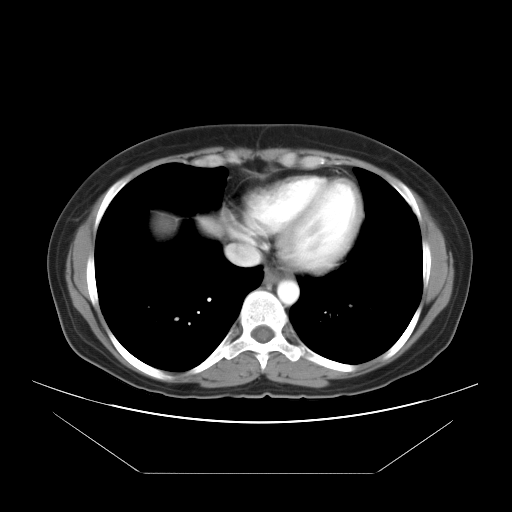
Contrast-enhanced abdominal CT, one axial slice; slice 34 of 34 in the series (ordered by position); reconstruction kernel STANDARD; 120 kVp; intravenous contrast given; soft-tissue window (W 400 / L 40 HU); 7.5 mm slice thickness; 512 × 512 image matrix. Female patient, age 38 years. From the clinical record (not read from this slice): diagnosis: colorectal cancer liver metastases, imaged before liver resection; multiple liver metastases: yes; largest metastasis: 3.1 cm.
Structures marked on this image (manually delineated by an expert):
- liver: bounding box (x1, y1, x2, y2) in pixels: (147, 213, 180, 240)